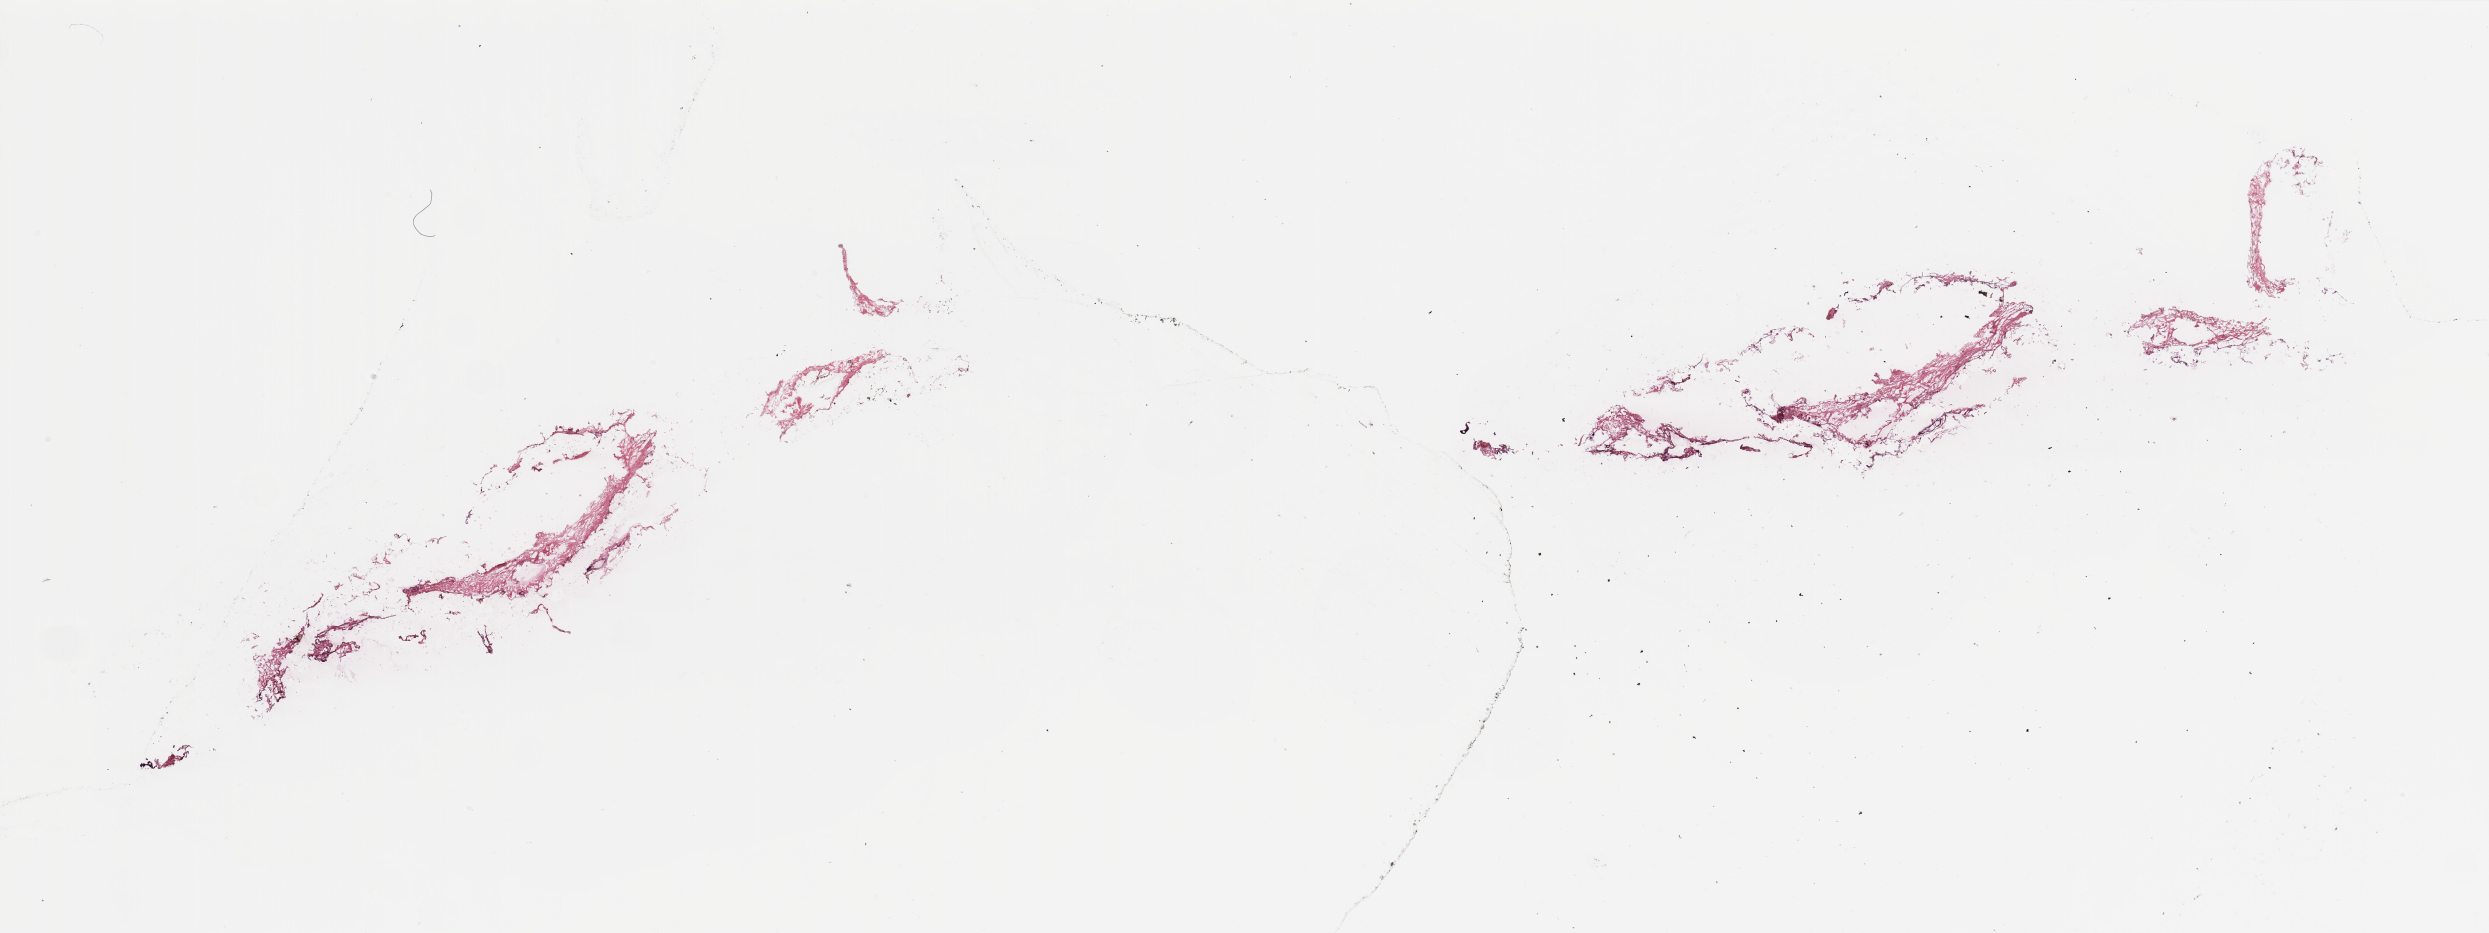
Whole-slide histology image, Hematoxylin and eosin (H&E) stained — whole scanned area (about 39.4 x 14.8 mm, from a 20x scan) shown as a low-resolution overview, tumour tissue sample, breast. Patient: female, age 58 years.
- diagnosis: Infiltrating duct carcinoma, NOS
- AJCC pathologic stage: II